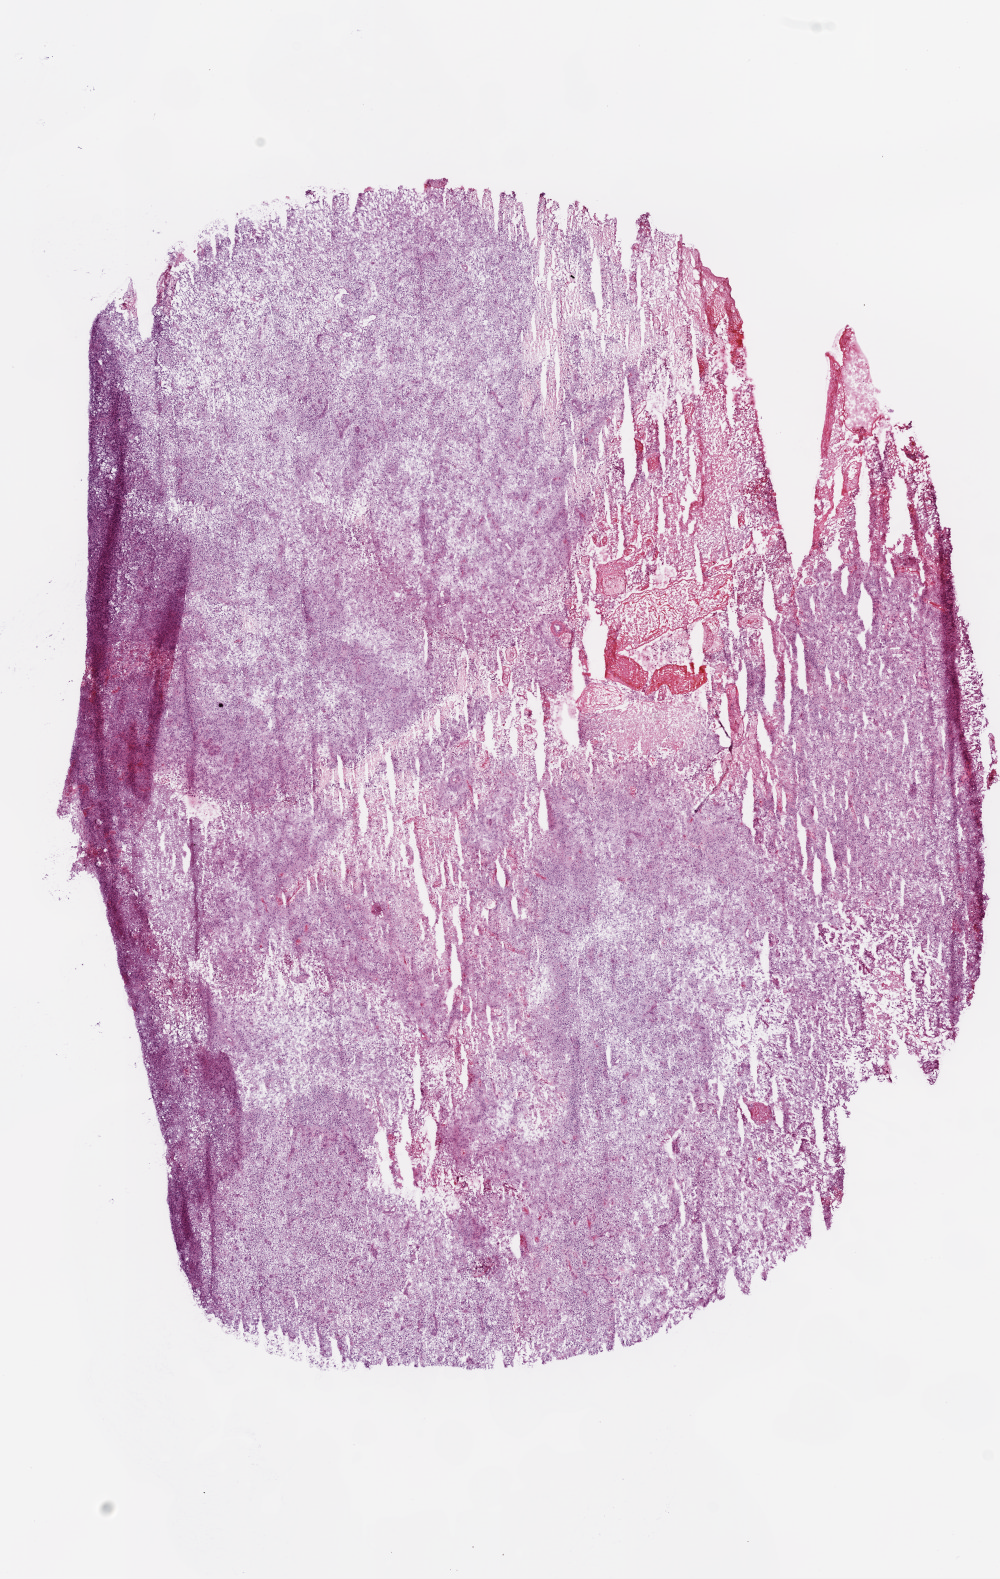
Digitized H&E-stained tissue section (whole slide) — low-resolution overview of the scanned area, about 8.0 x 12.7 mm (from a 20x scan). Frozen section from the bottom of the tissue portion. Primary tumour sample from the brain. Male patient; age at initial diagnosis 81 years. Pathologist review of this section (percent, as recorded): tumour cells 80%, tumour nuclei 80%, normal cells 0%, stromal cells 0%, necrosis 20%.
Histologic diagnosis: Glioblastoma.